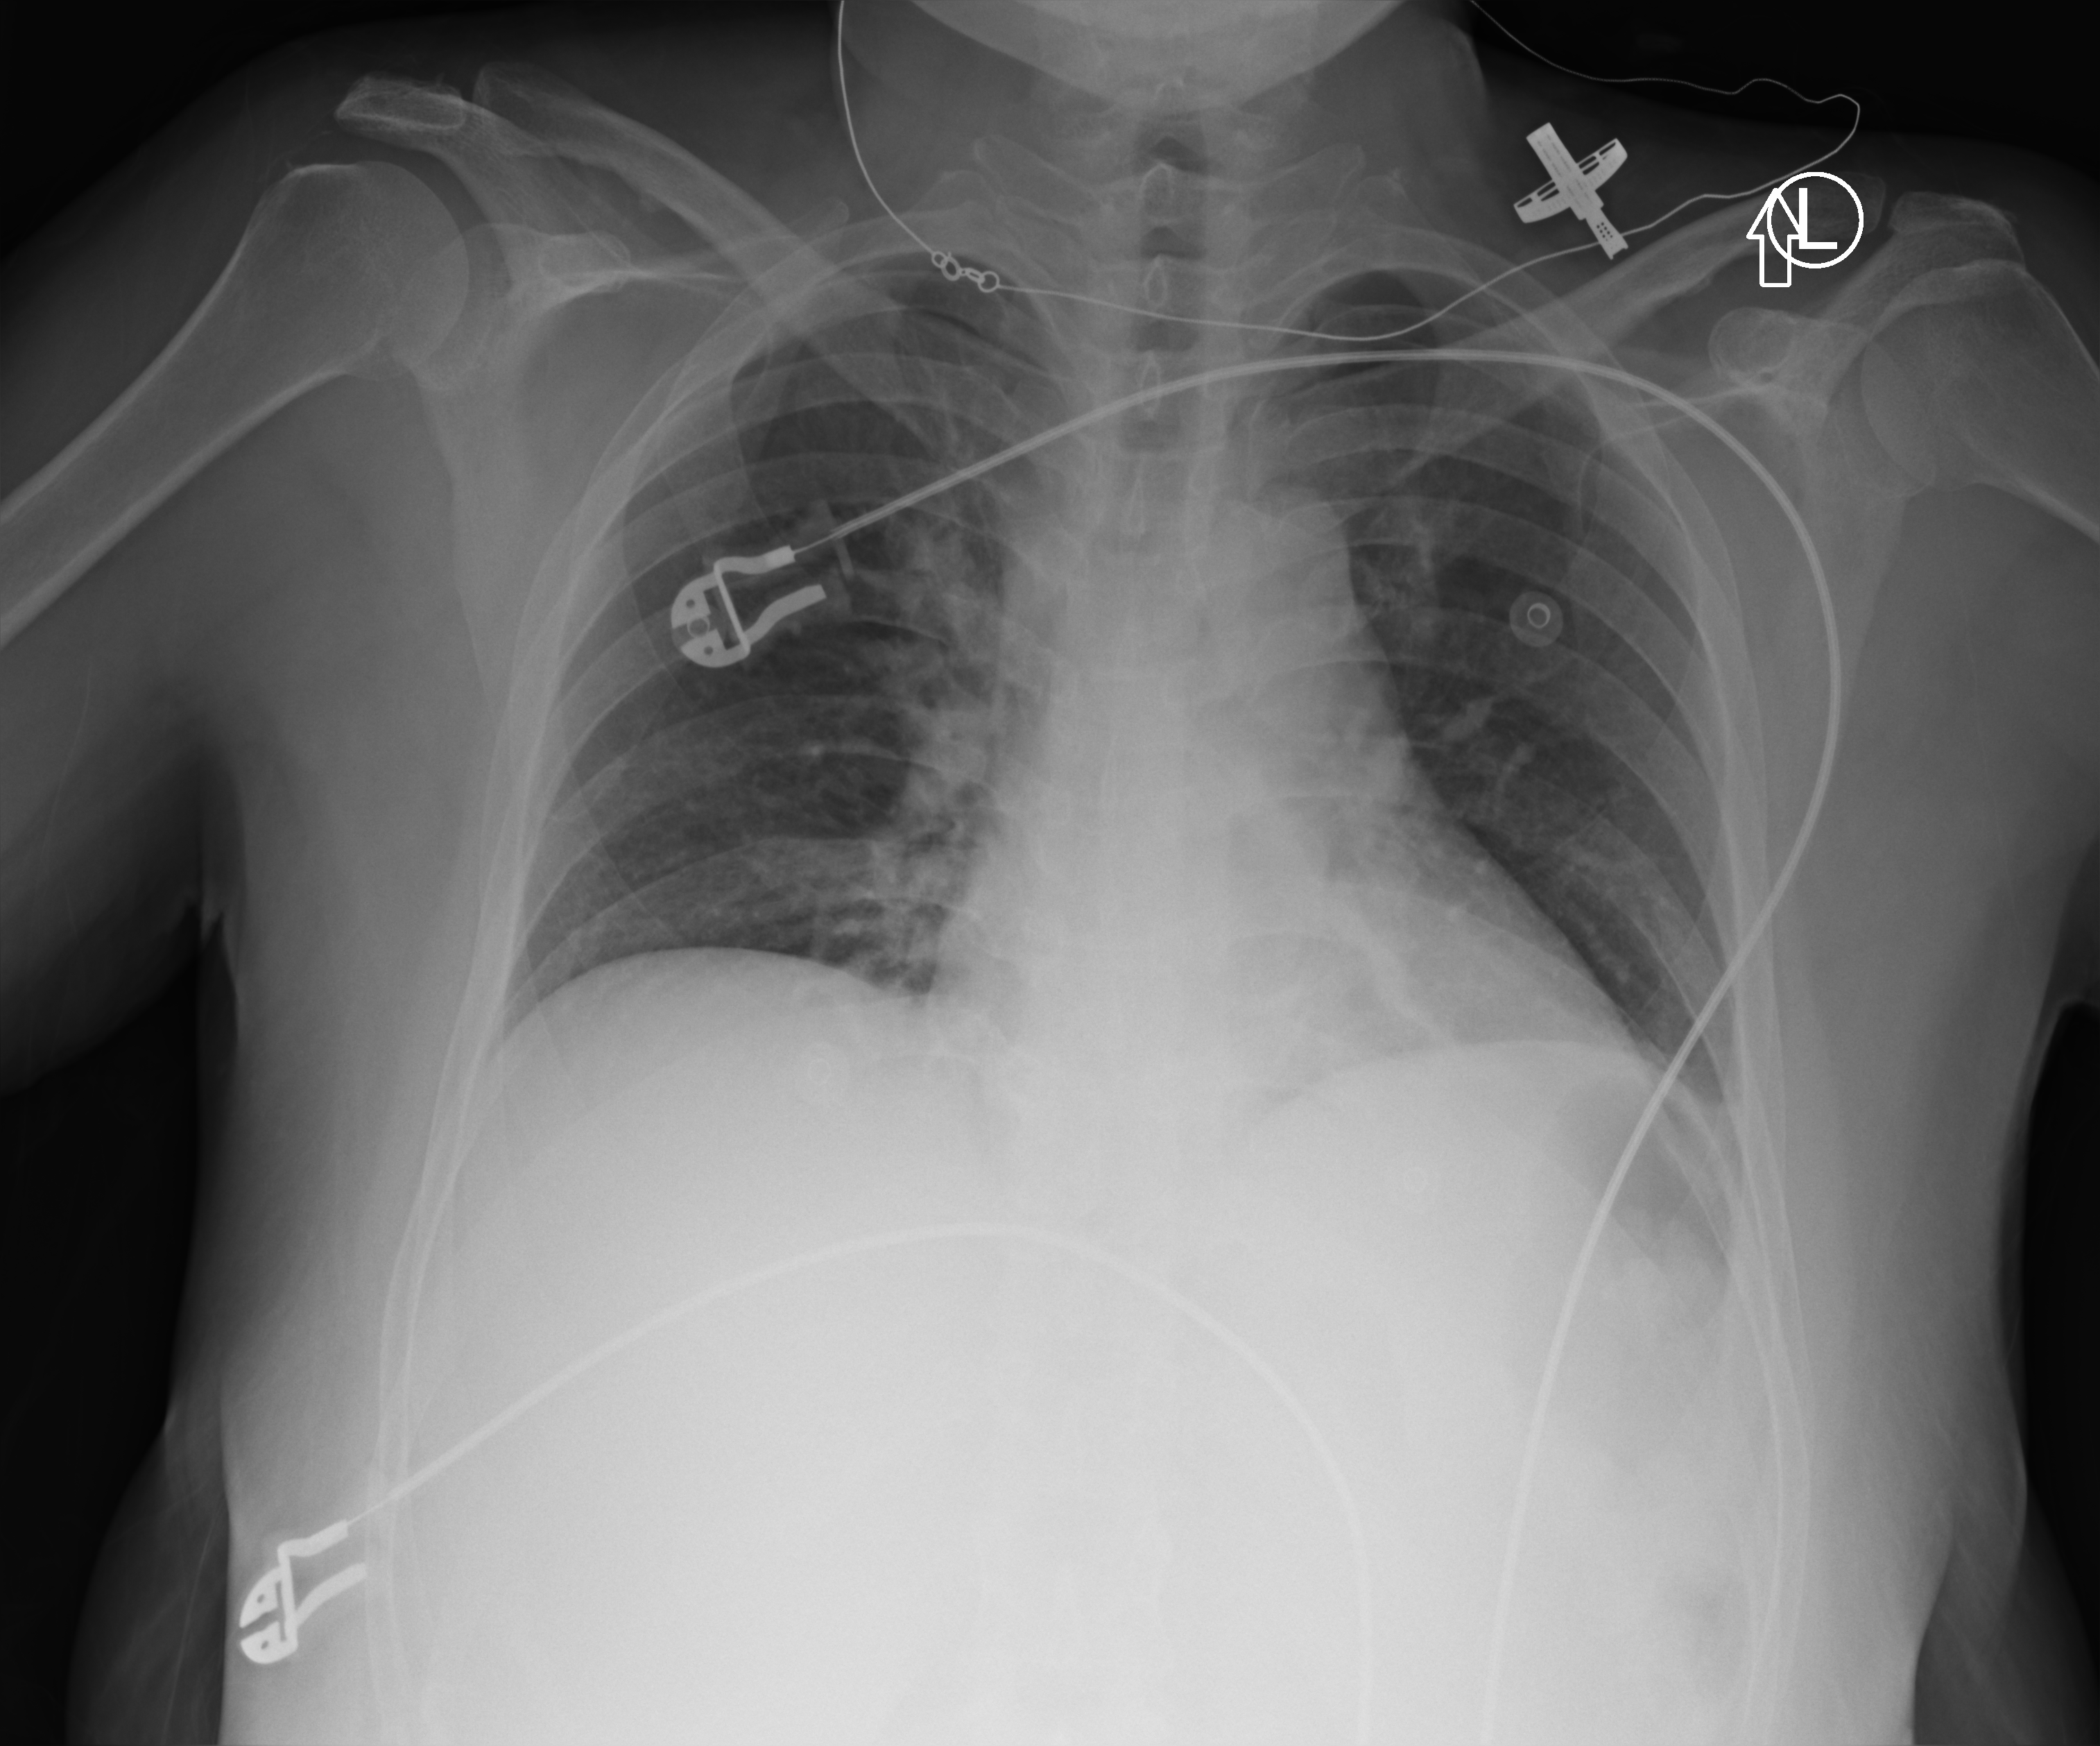
Bedside chest radiograph (computed radiography); anteroposterior (AP) projection. Patient hospitalised with COVID-19; female, aged 18–59 years.
From the hospital-stay record, not from the radiograph (when in the stay this image was taken is not recorded): COPD (admission record): no.